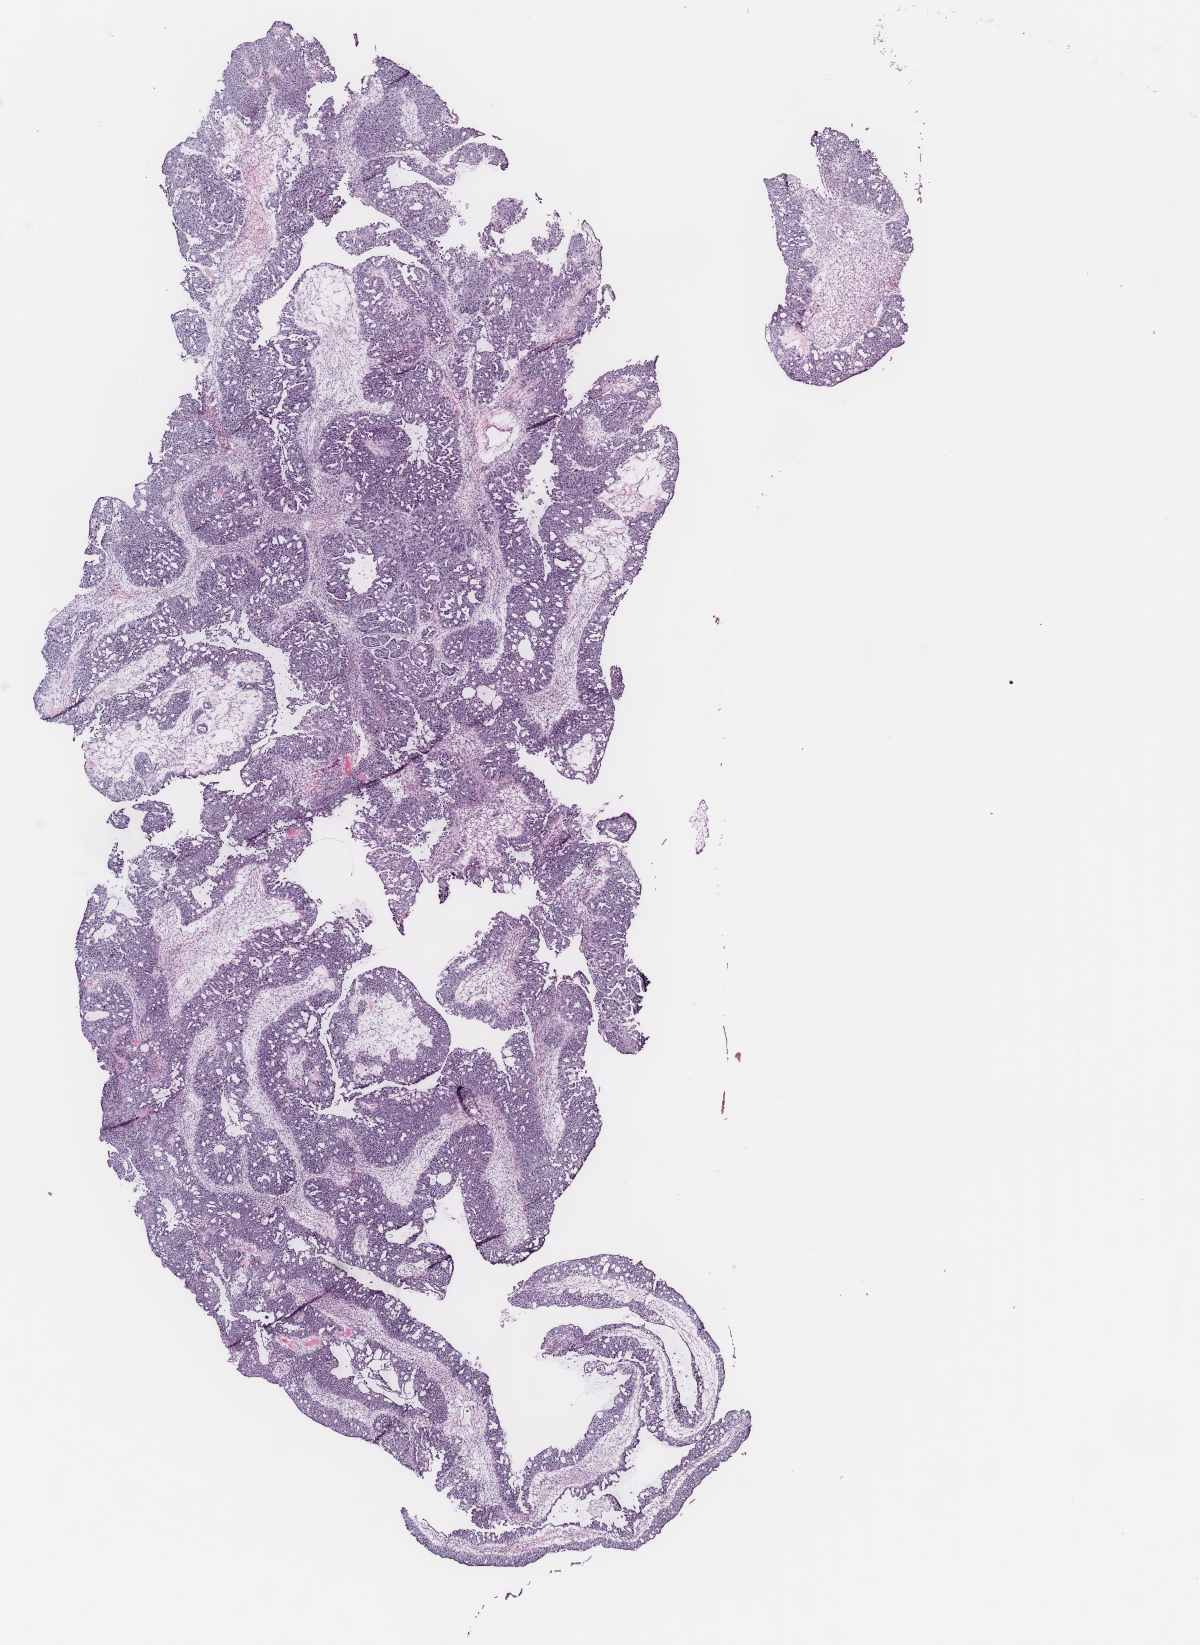
Digitized H&E tissue section (whole slide), low-resolution overview of the scanned area, about 9.6 x 13.2 mm, ovary, tumour tissue. 70-year-old female patient.
Primary tumour site (as recorded): ovary. Histologic diagnosis: Serous adenocarcinoma, NOS.